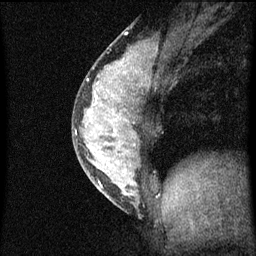
Breast MRI (dynamic contrast-enhanced), one sagittal slice. Slice 27 of 60 in the series (ordered by position). Dynamic contrast-enhanced series, image 2 of 3 at this slice position (ordered by acquisition). 1.5 T. TE 4.2 ms, TR 8 ms. 2 mm slice thickness. 256 × 256 image matrix, field of view 180 × 180 mm. Patient: female, 33 years.
Outlined on this slice (semi-automatic segmentation, software-assisted and operator-edited):
- analysis volume of interest (the breast-tissue region the enhancement analysis was run in; not a lesion): bounding box <72,56,157,211> (left, top, right, bottom; pixels)
- tumour enhancement mask (voxels above the 70 % enhancement threshold inside the analysis volume of interest): <76,56,147,195>